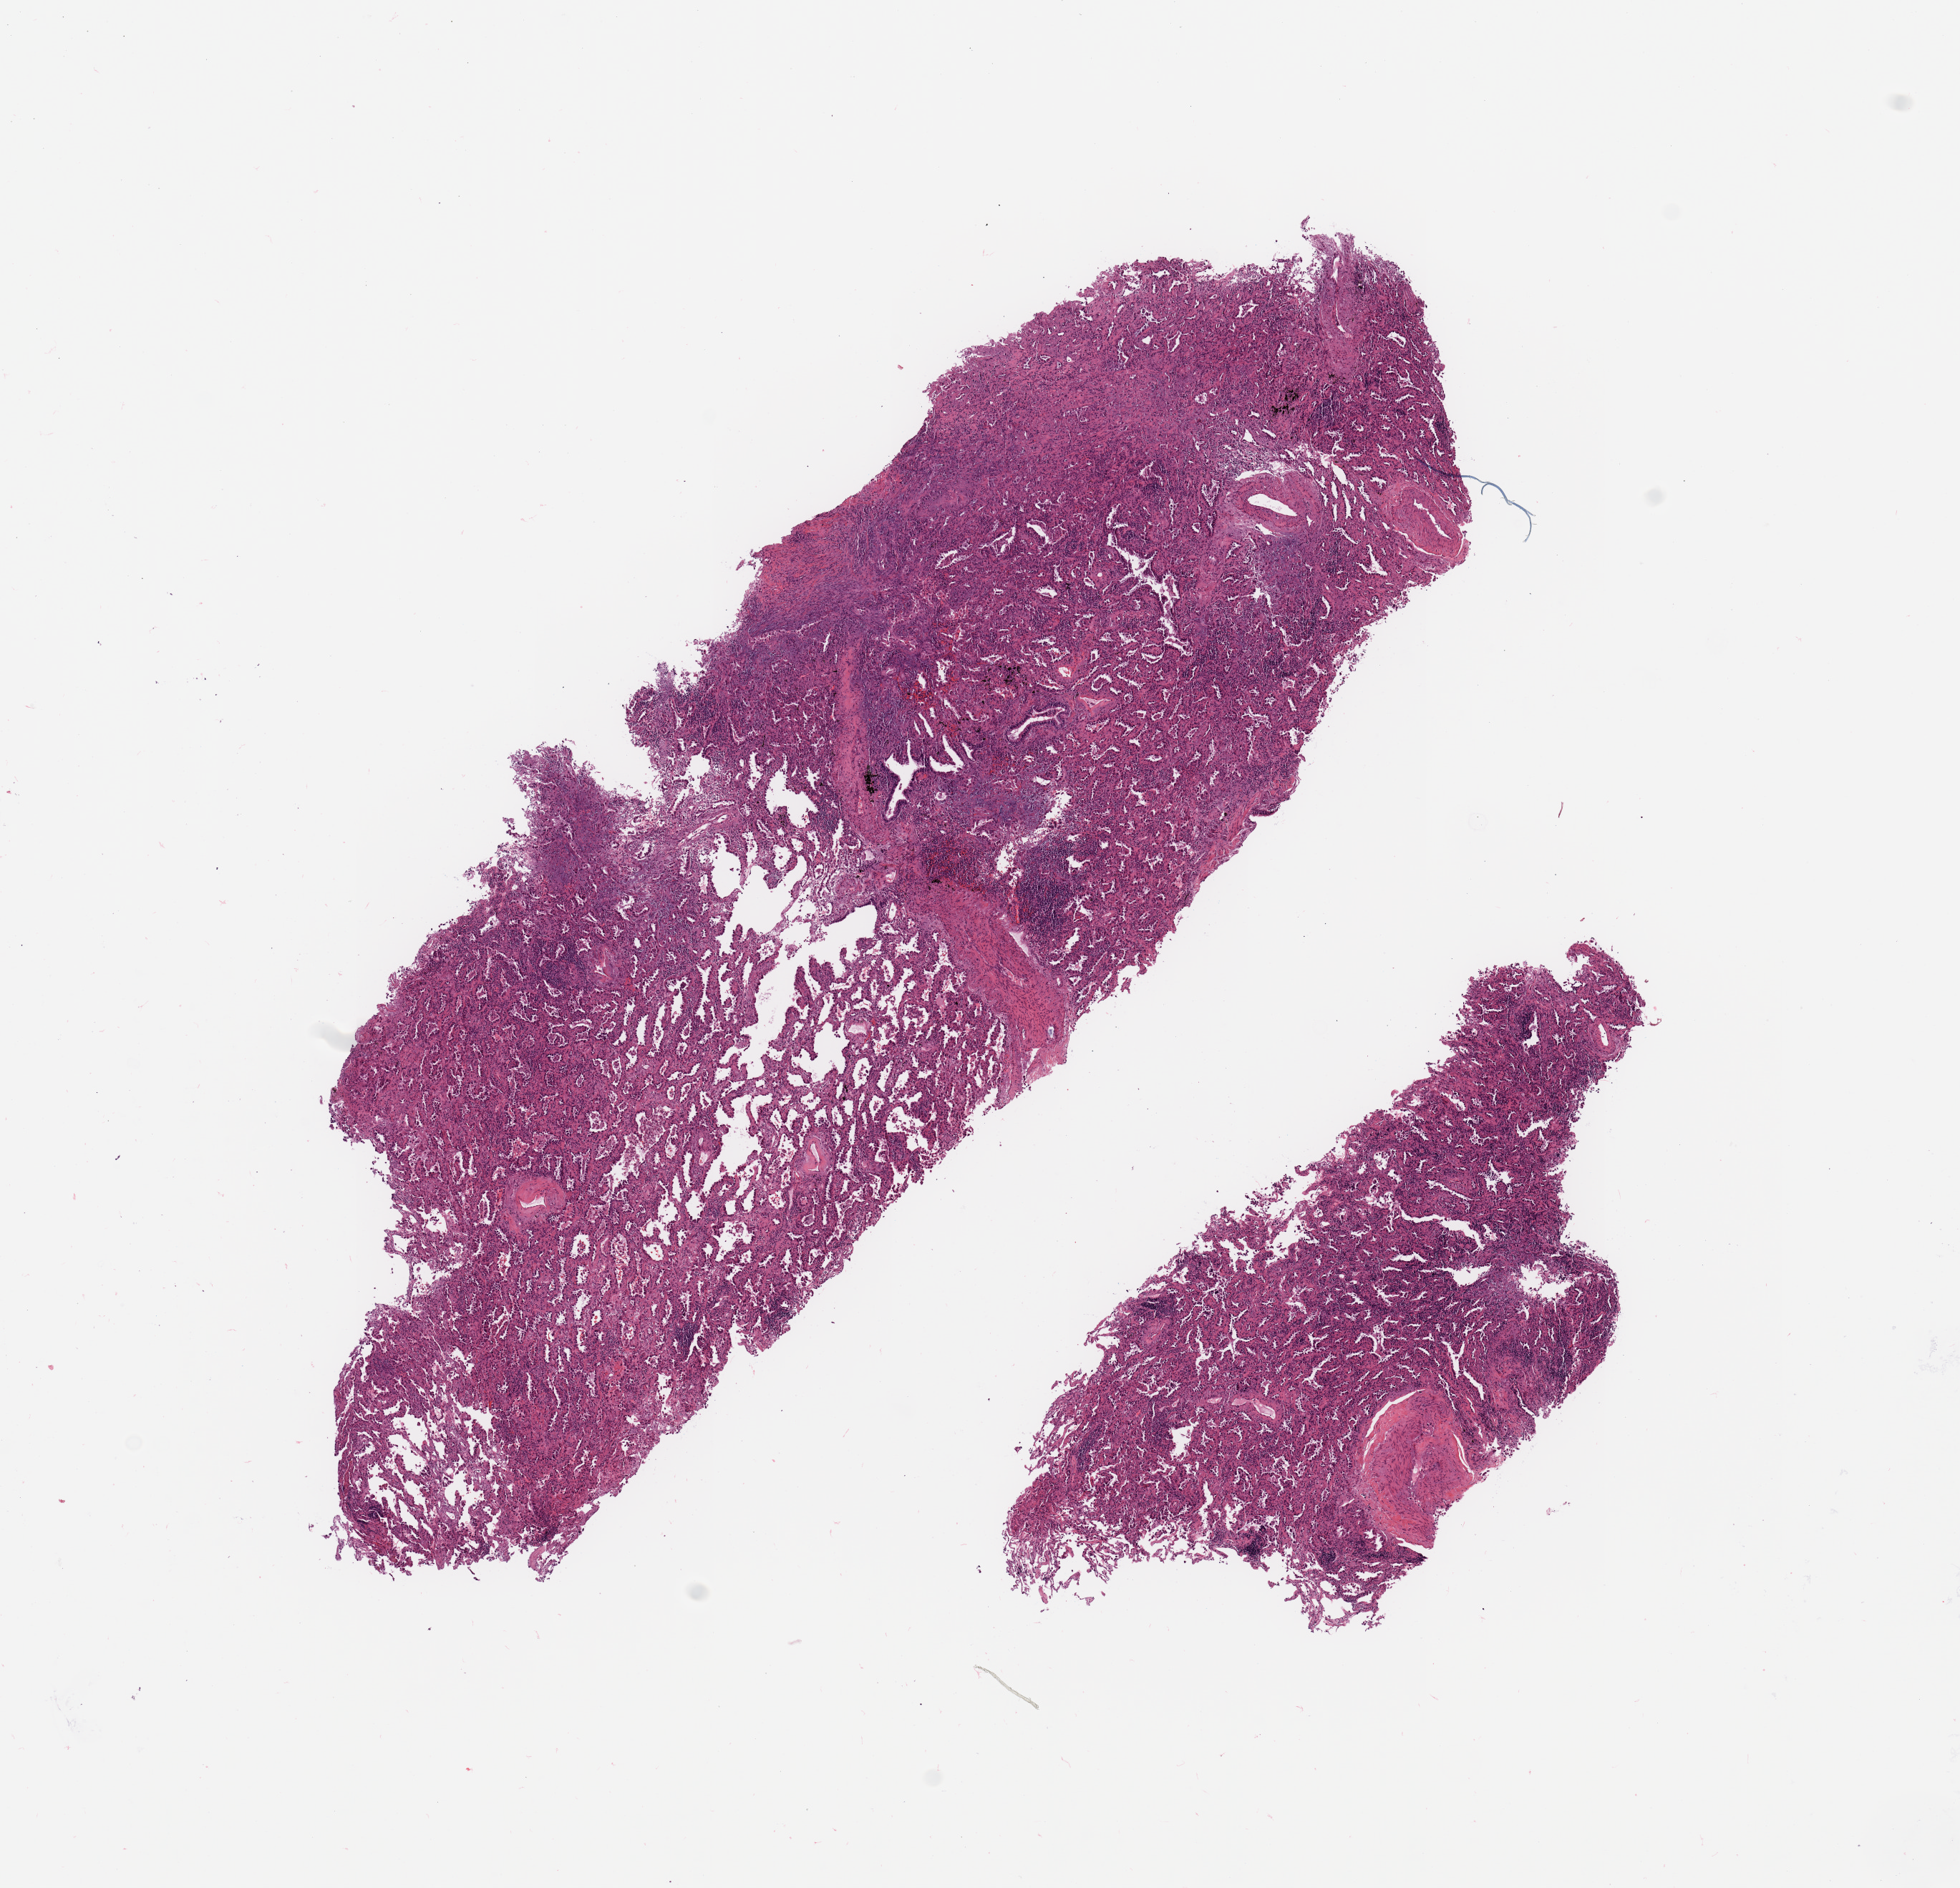
Whole-slide histology image, Hematoxylin and eosin (H&E) stained — whole scanned area (about 10.8 x 10.4 mm) shown as a low-resolution overview. Tumour tissue sample, sampled site: lung. Female, 70 y/o. Histologic grade: GX (grade cannot be assessed). Composition of this section per pathologist review: tumour nuclei 80%, necrosis 0%.
- AJCC pathologic stage: IB
- diagnosis: Adenocarcinoma, NOS